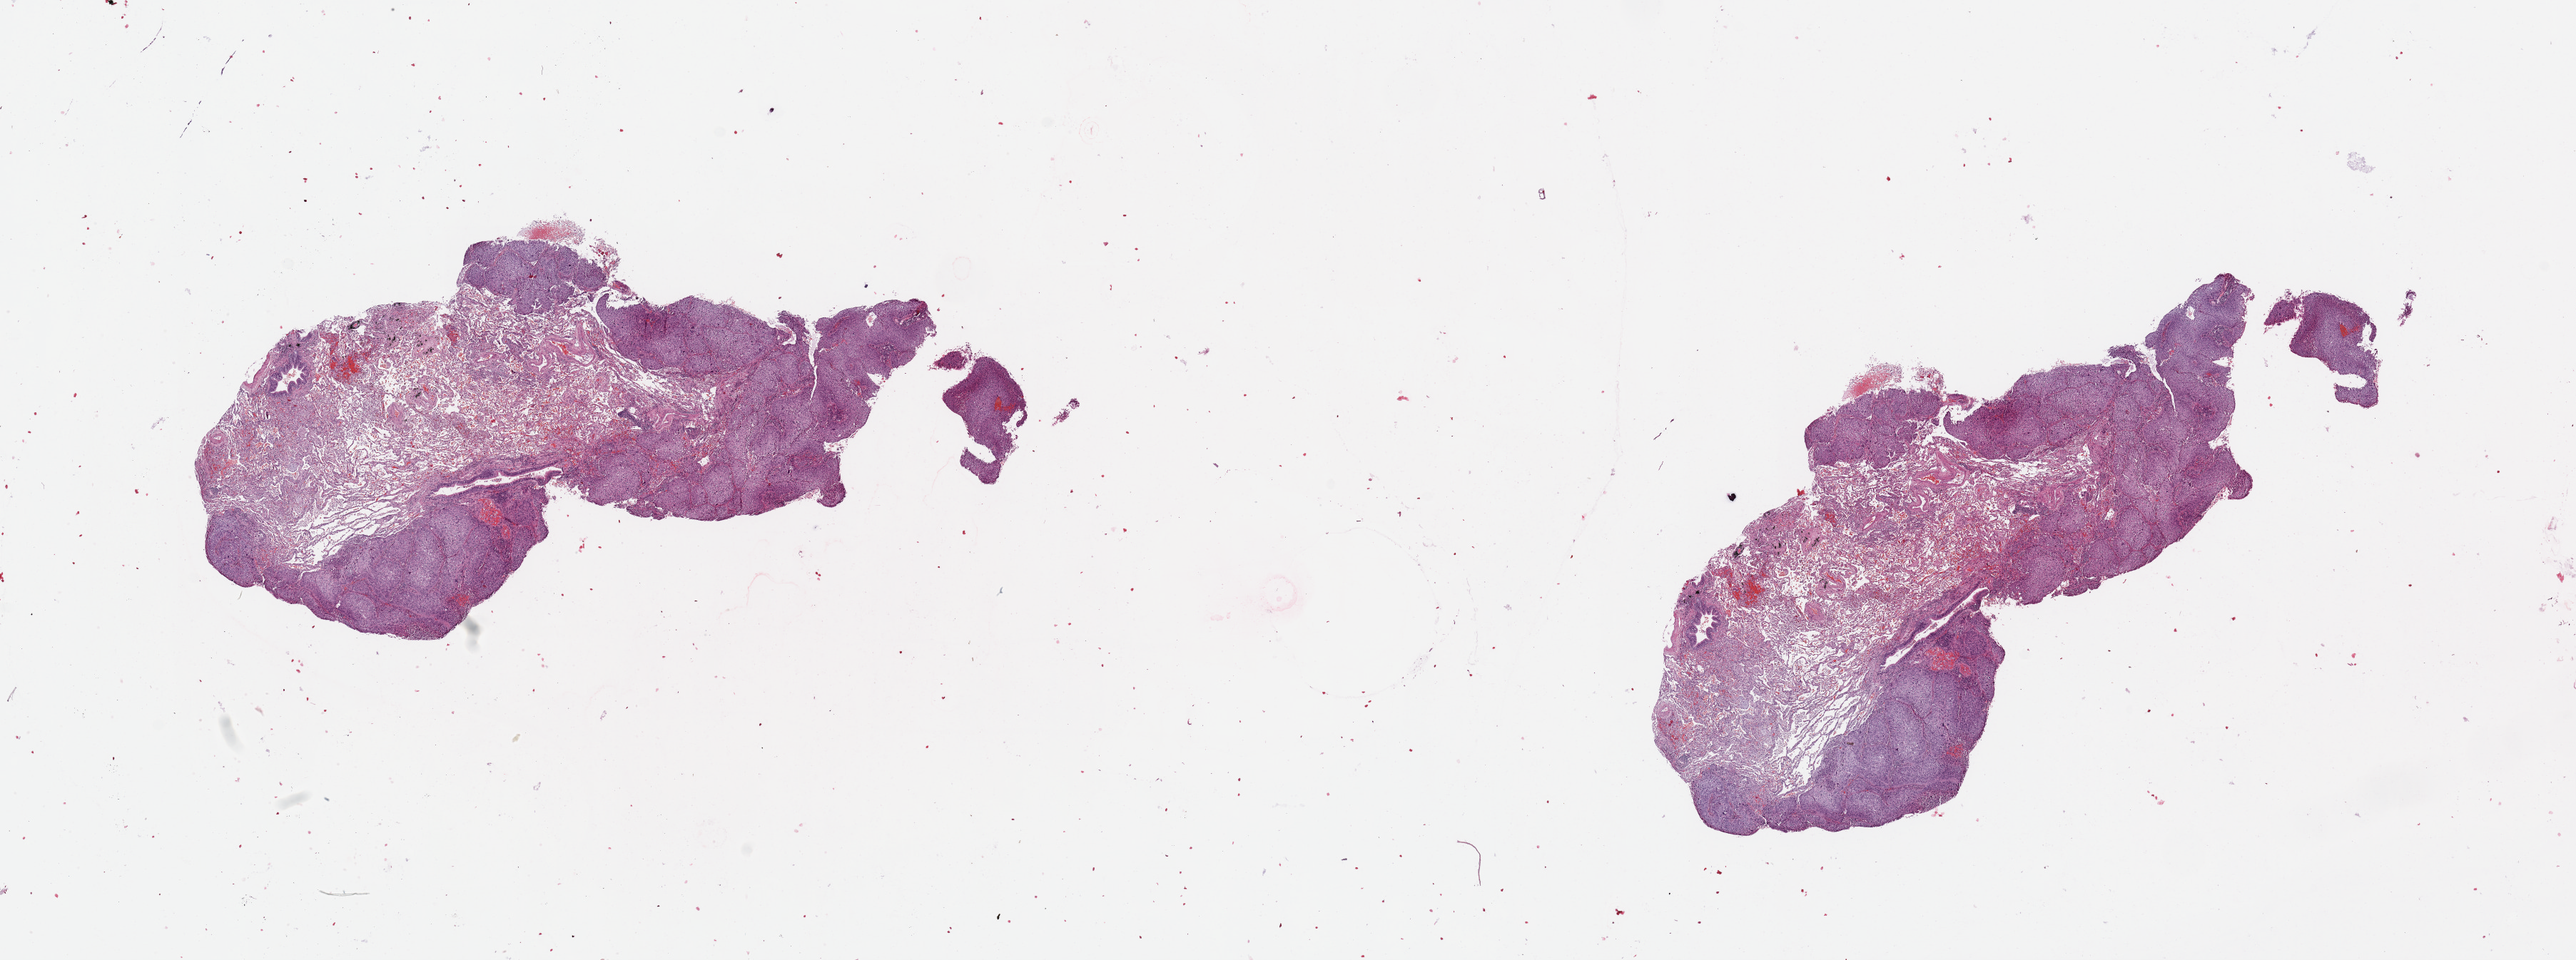
Digitized H&E-stained tissue section (whole slide) — whole scanned area (about 28.5 x 10.6 mm) shown as a low-resolution overview, lung, tumour tissue. Female, 64 y/o. Histologic grade: G3 (poorly differentiated).
Histologic diagnosis: Squamous cell carcinoma, NOS. Primary tumour site (as recorded): right lower lobe. AJCC pathologic stage: IA.